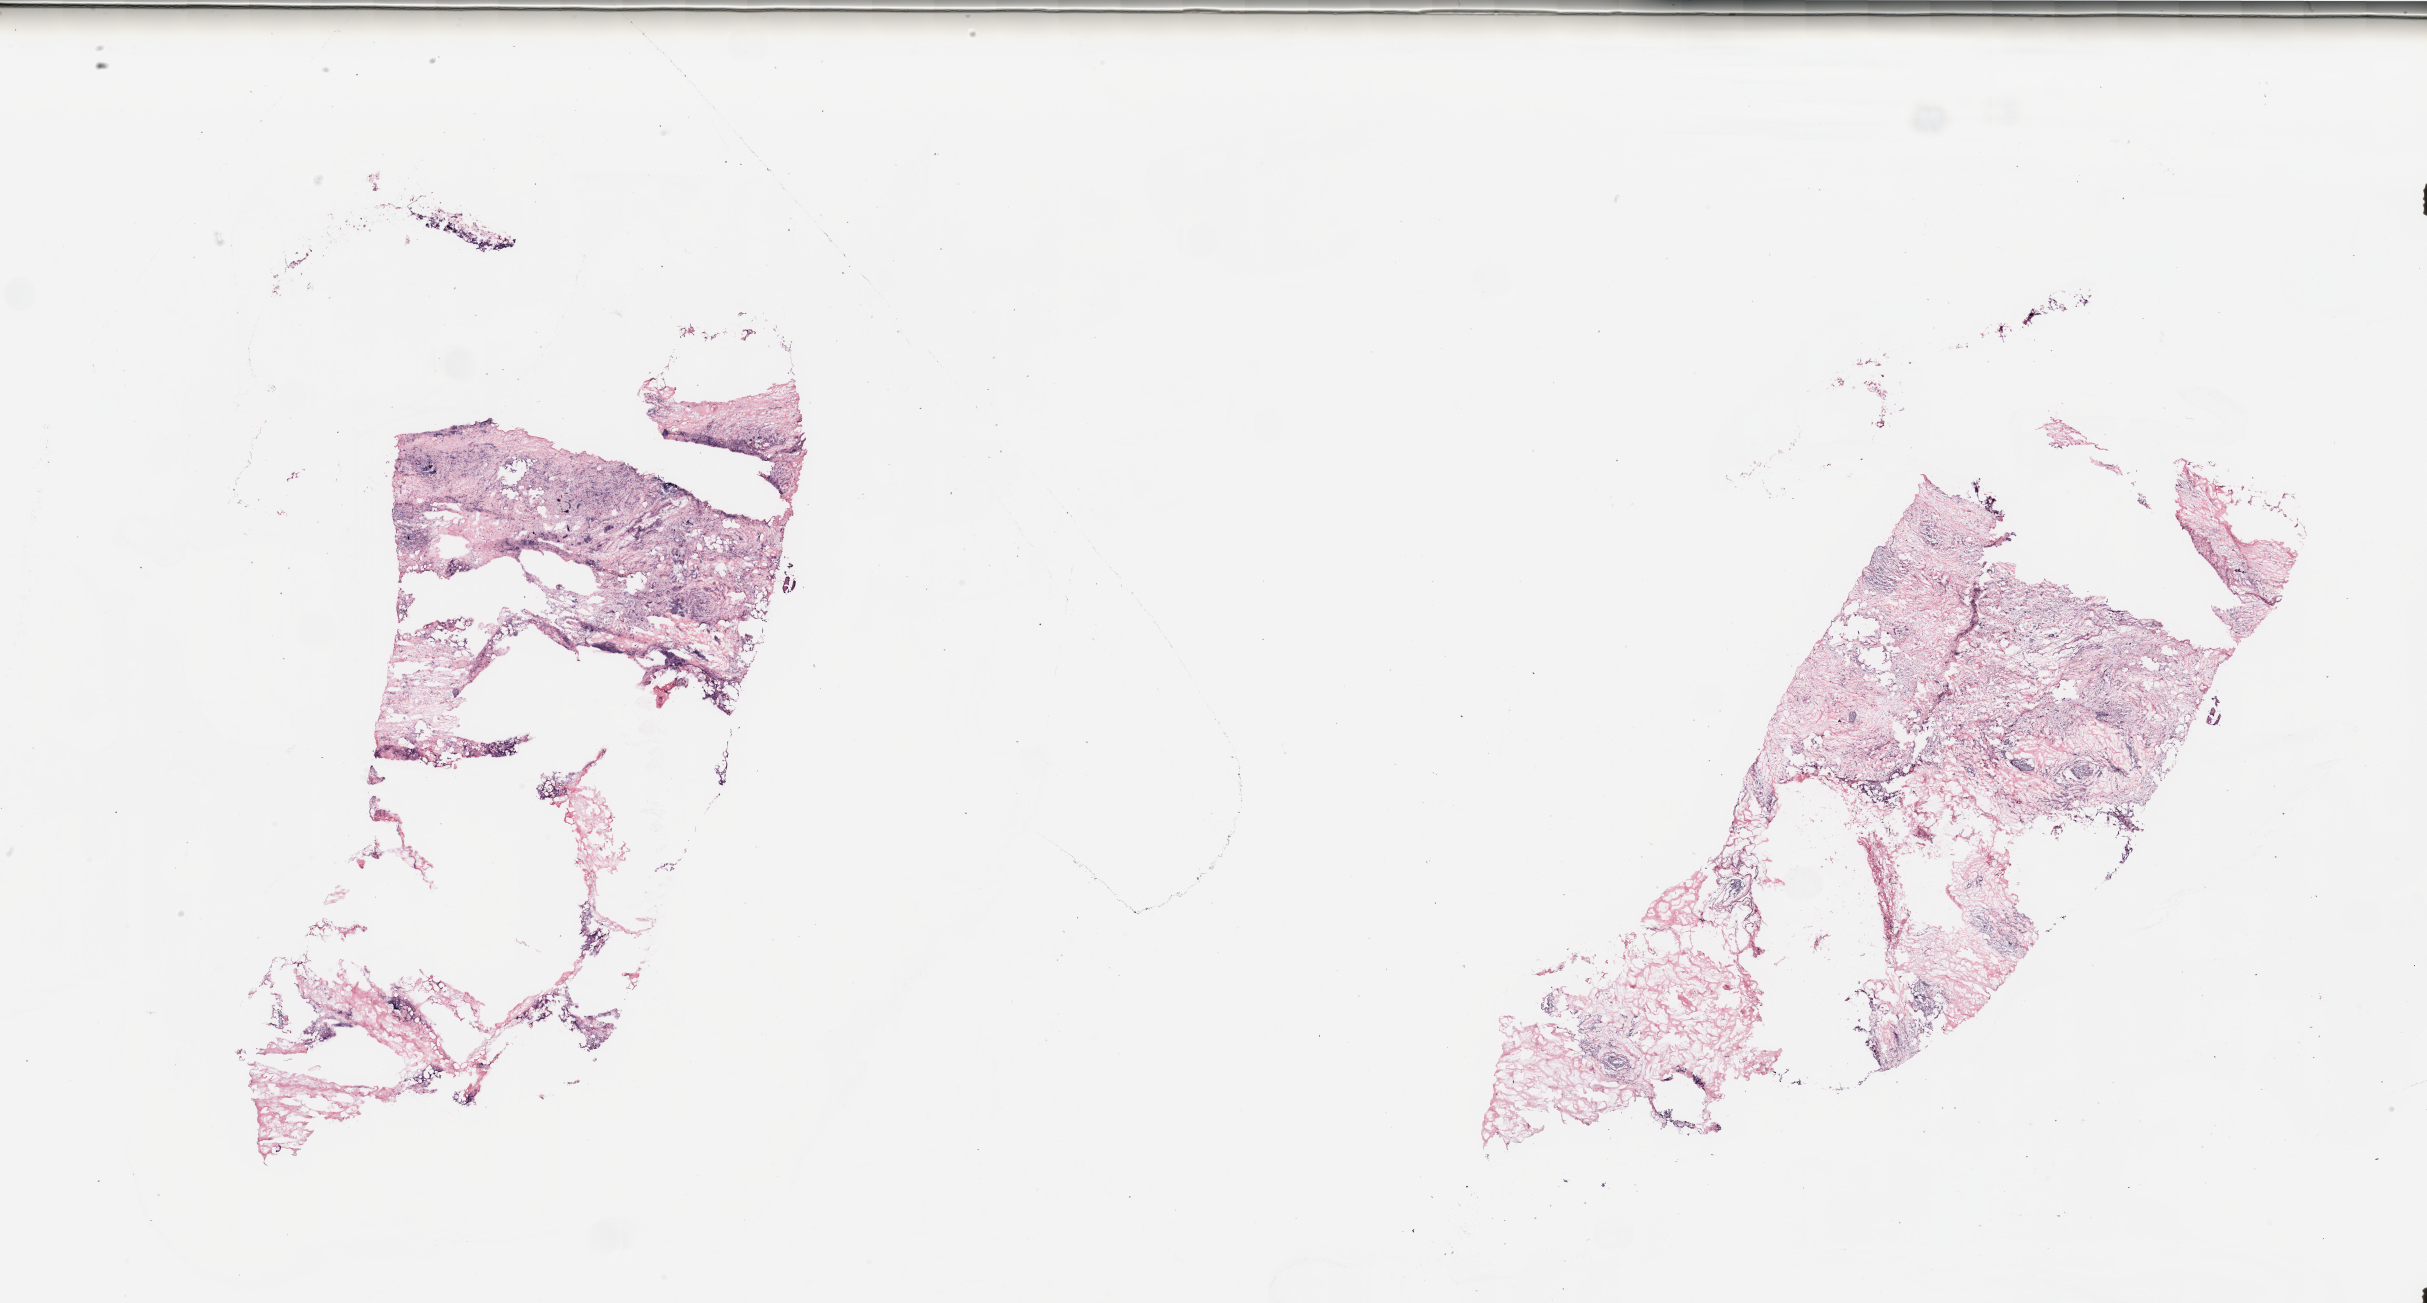
H&E-stained whole-slide image, whole scanned area (about 38.4 x 20.6 mm, from a 20x scan) shown as a low-resolution overview; breast, tissue type not recorded.
Patient diagnosis (cohort enrolment): breast cancer (breast).